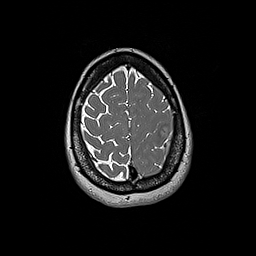
Brain MRI from a brain-tumour surgery series, one axial slice; position 51 of 192 along the scan axis; 1 mm slice thickness; 256 × 256 image matrix, field of view 250 × 250 mm. Case-level facts recorded for this patient, not image findings: histopathology: Glioblastoma; WHO grade: 4; IDH mutation: no.
Annotated regions visible in this slice (outlined manually by an expert reader):
- tumour: box from (x=160, y=127) to (x=183, y=159) px